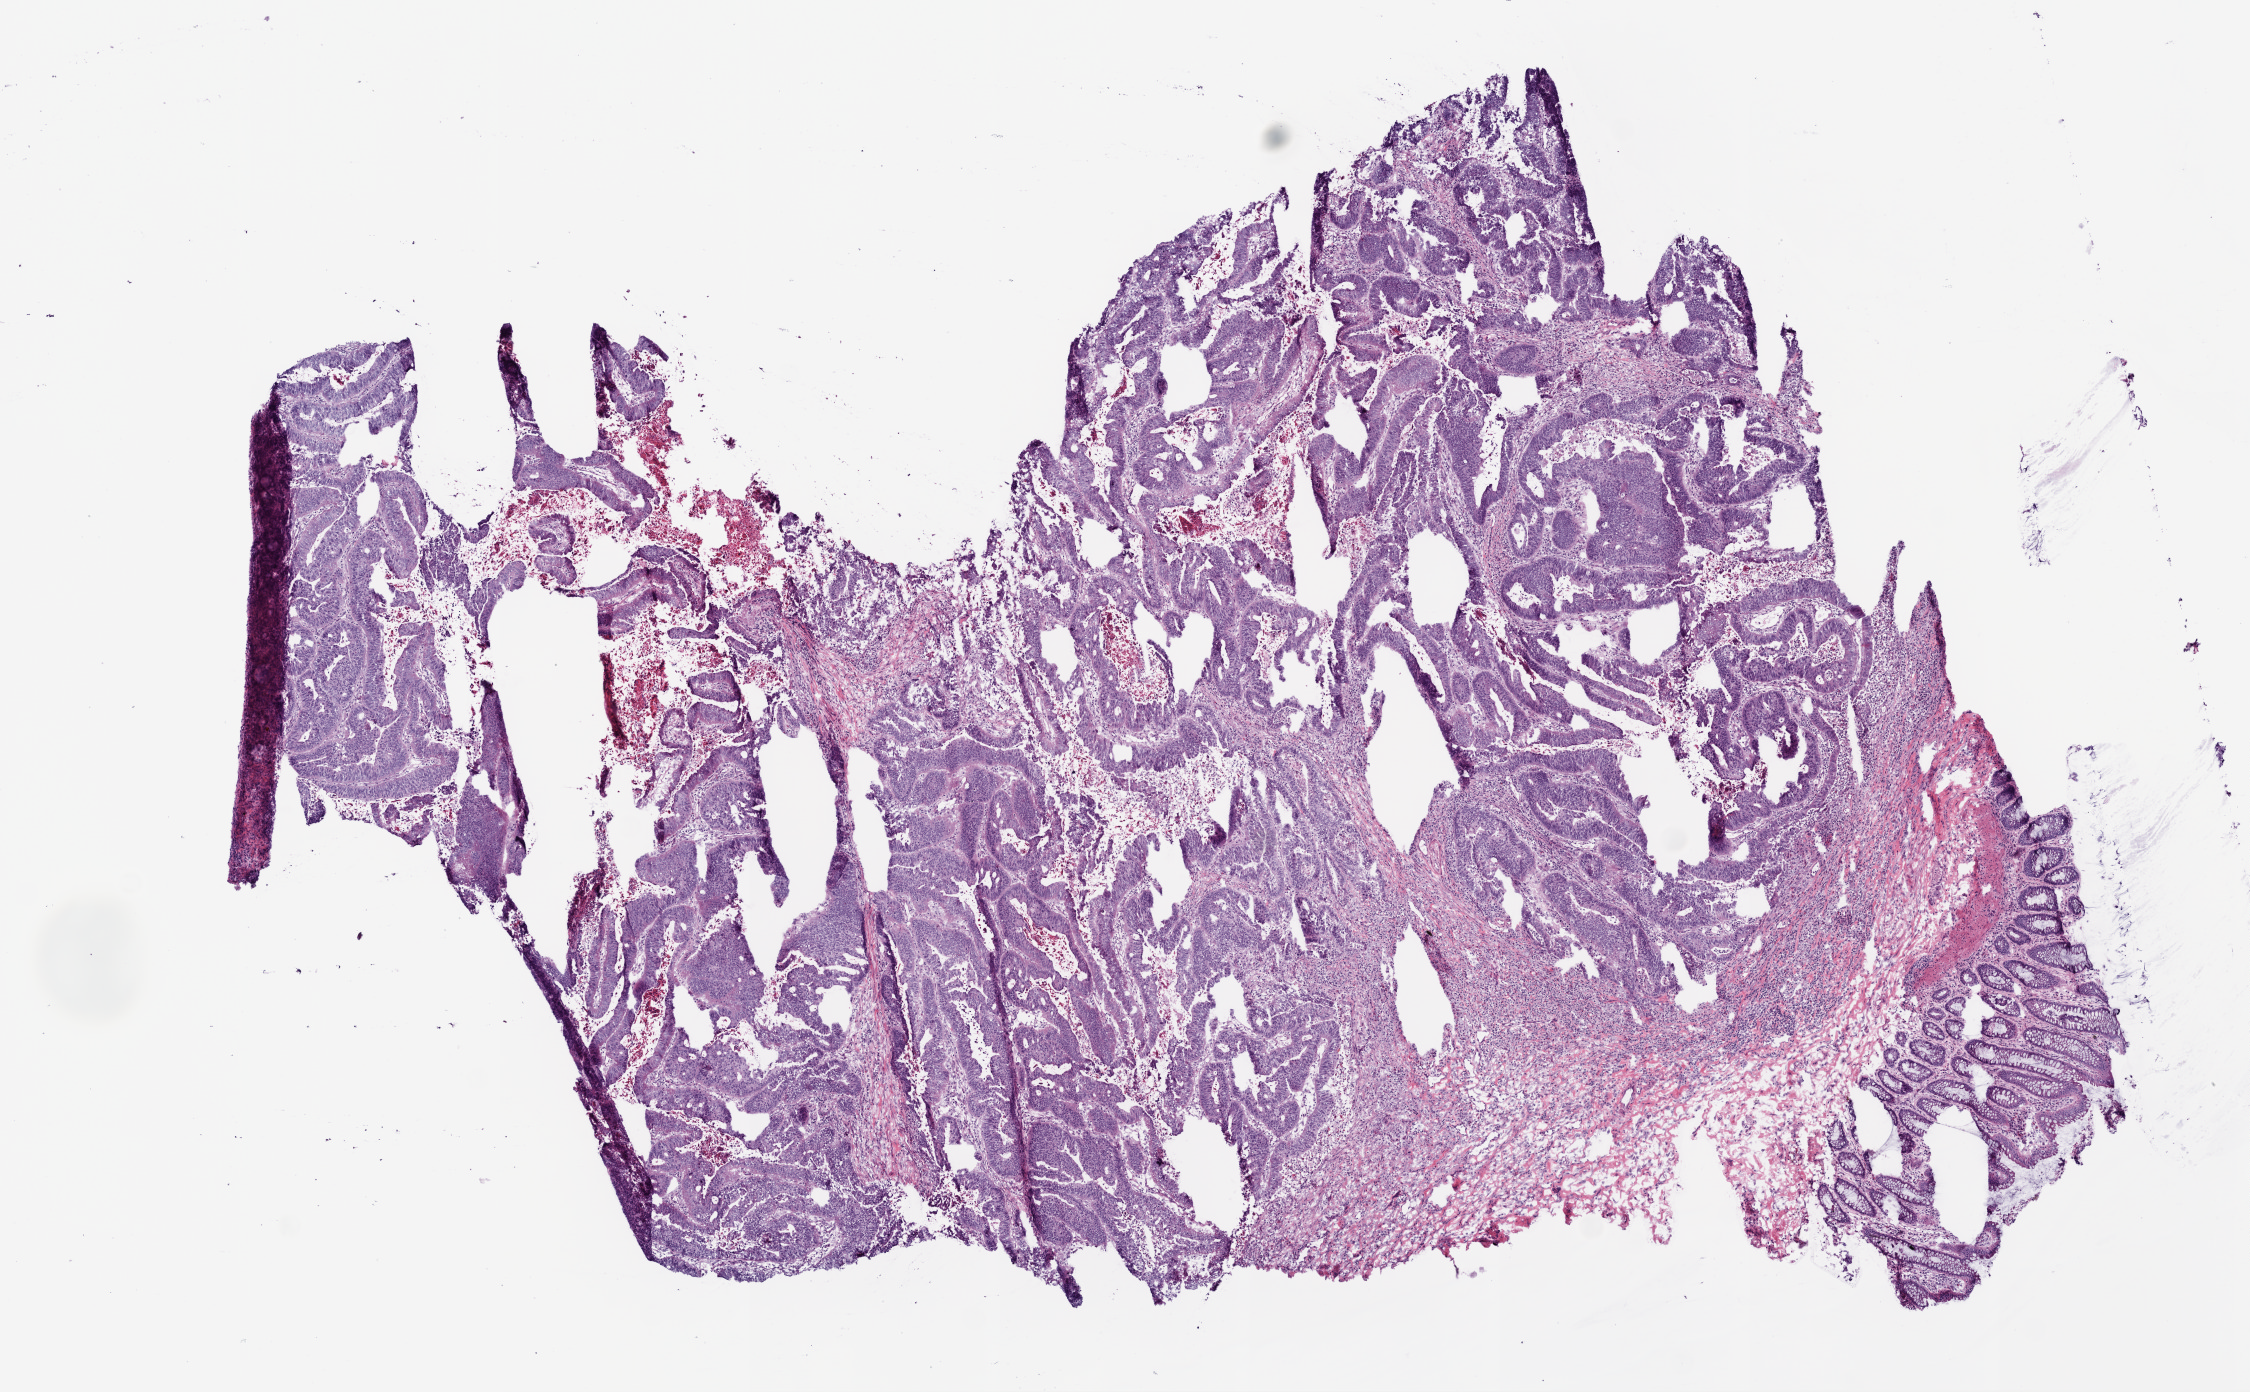
Digitized H&E tissue section (whole slide), low-resolution overview of the scanned area, about 9.0 x 5.6 mm (slide scanned at 20x). Frozen section. Rectum, primary tumour sample. Female patient; age at initial diagnosis 66 years.
Pathologic diagnosis: Adenocarcinoma, NOS.